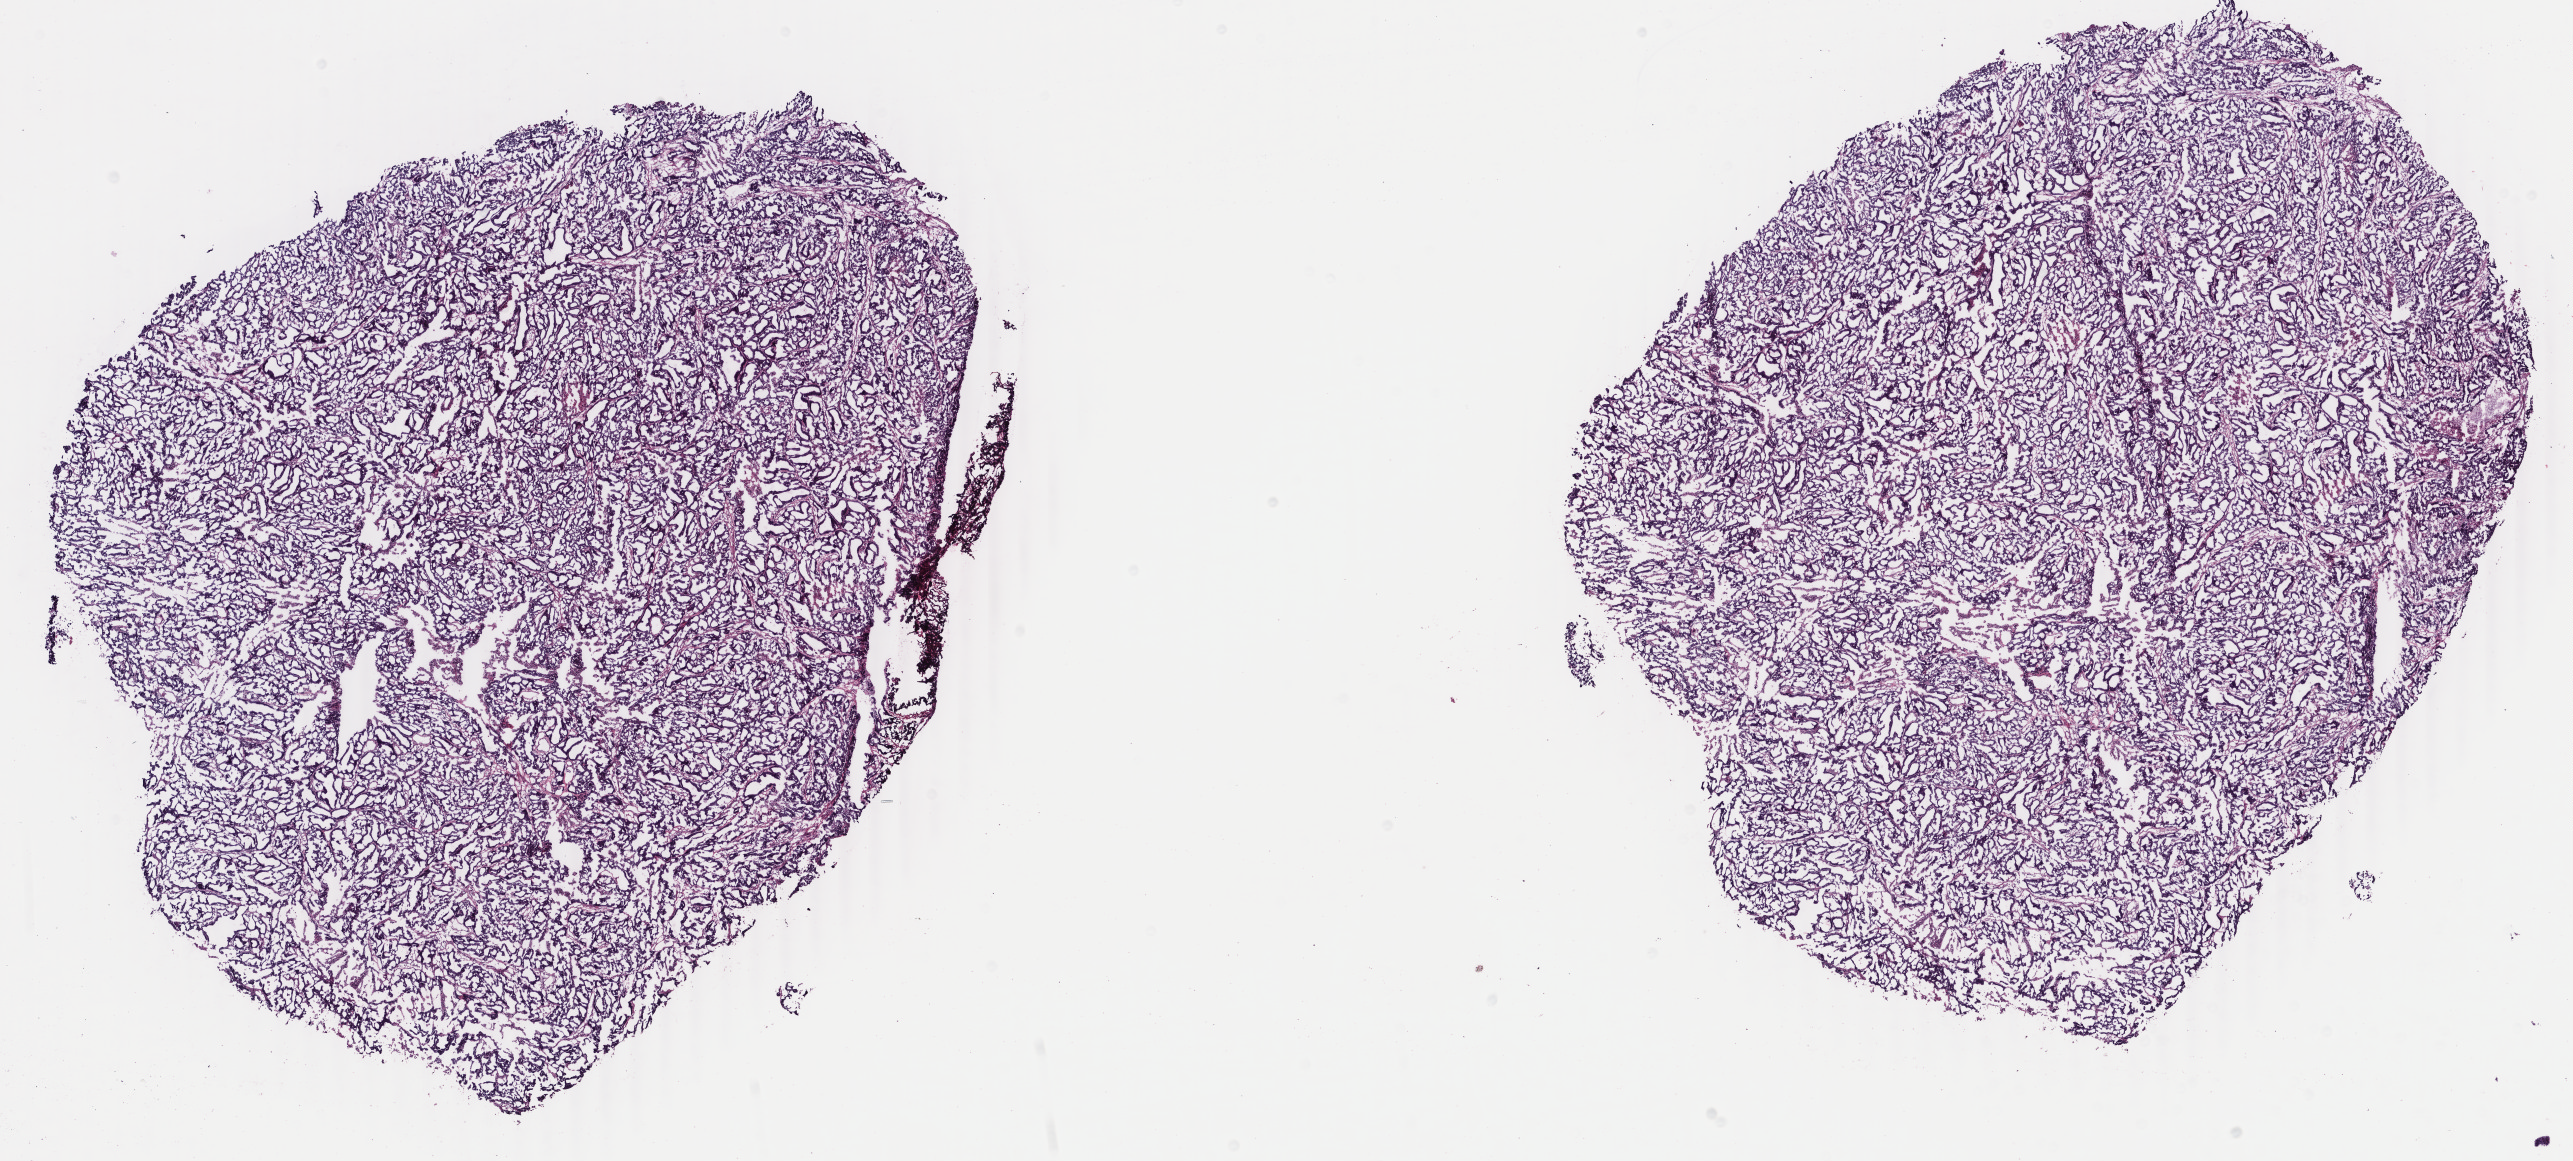
H&E whole-slide image — shown as a low-resolution overview of the whole scanned area (about 20.5 x 9.2 mm, slide scanned at 40x). Frozen section from the bottom of the tissue portion. Sample: primary tumour, uterus. Female patient; age at initial diagnosis 57 years. Histologic grade: G2 (moderately differentiated). Composition of this section per pathologist review: tumour cells 95%, tumour nuclei 90%, normal cells 0%, stromal cells 0%, necrosis 5%. Inflammatory infiltration, as recorded: lymphocyte infiltration 0%, monocyte infiltration 0%, neutrophil infiltration 0%.
• diagnosis: Endometrioid adenocarcinoma, NOS (endometrium)
• lymph nodes positive (case pathology): 0 of 16 examined
• FIGO stage: II